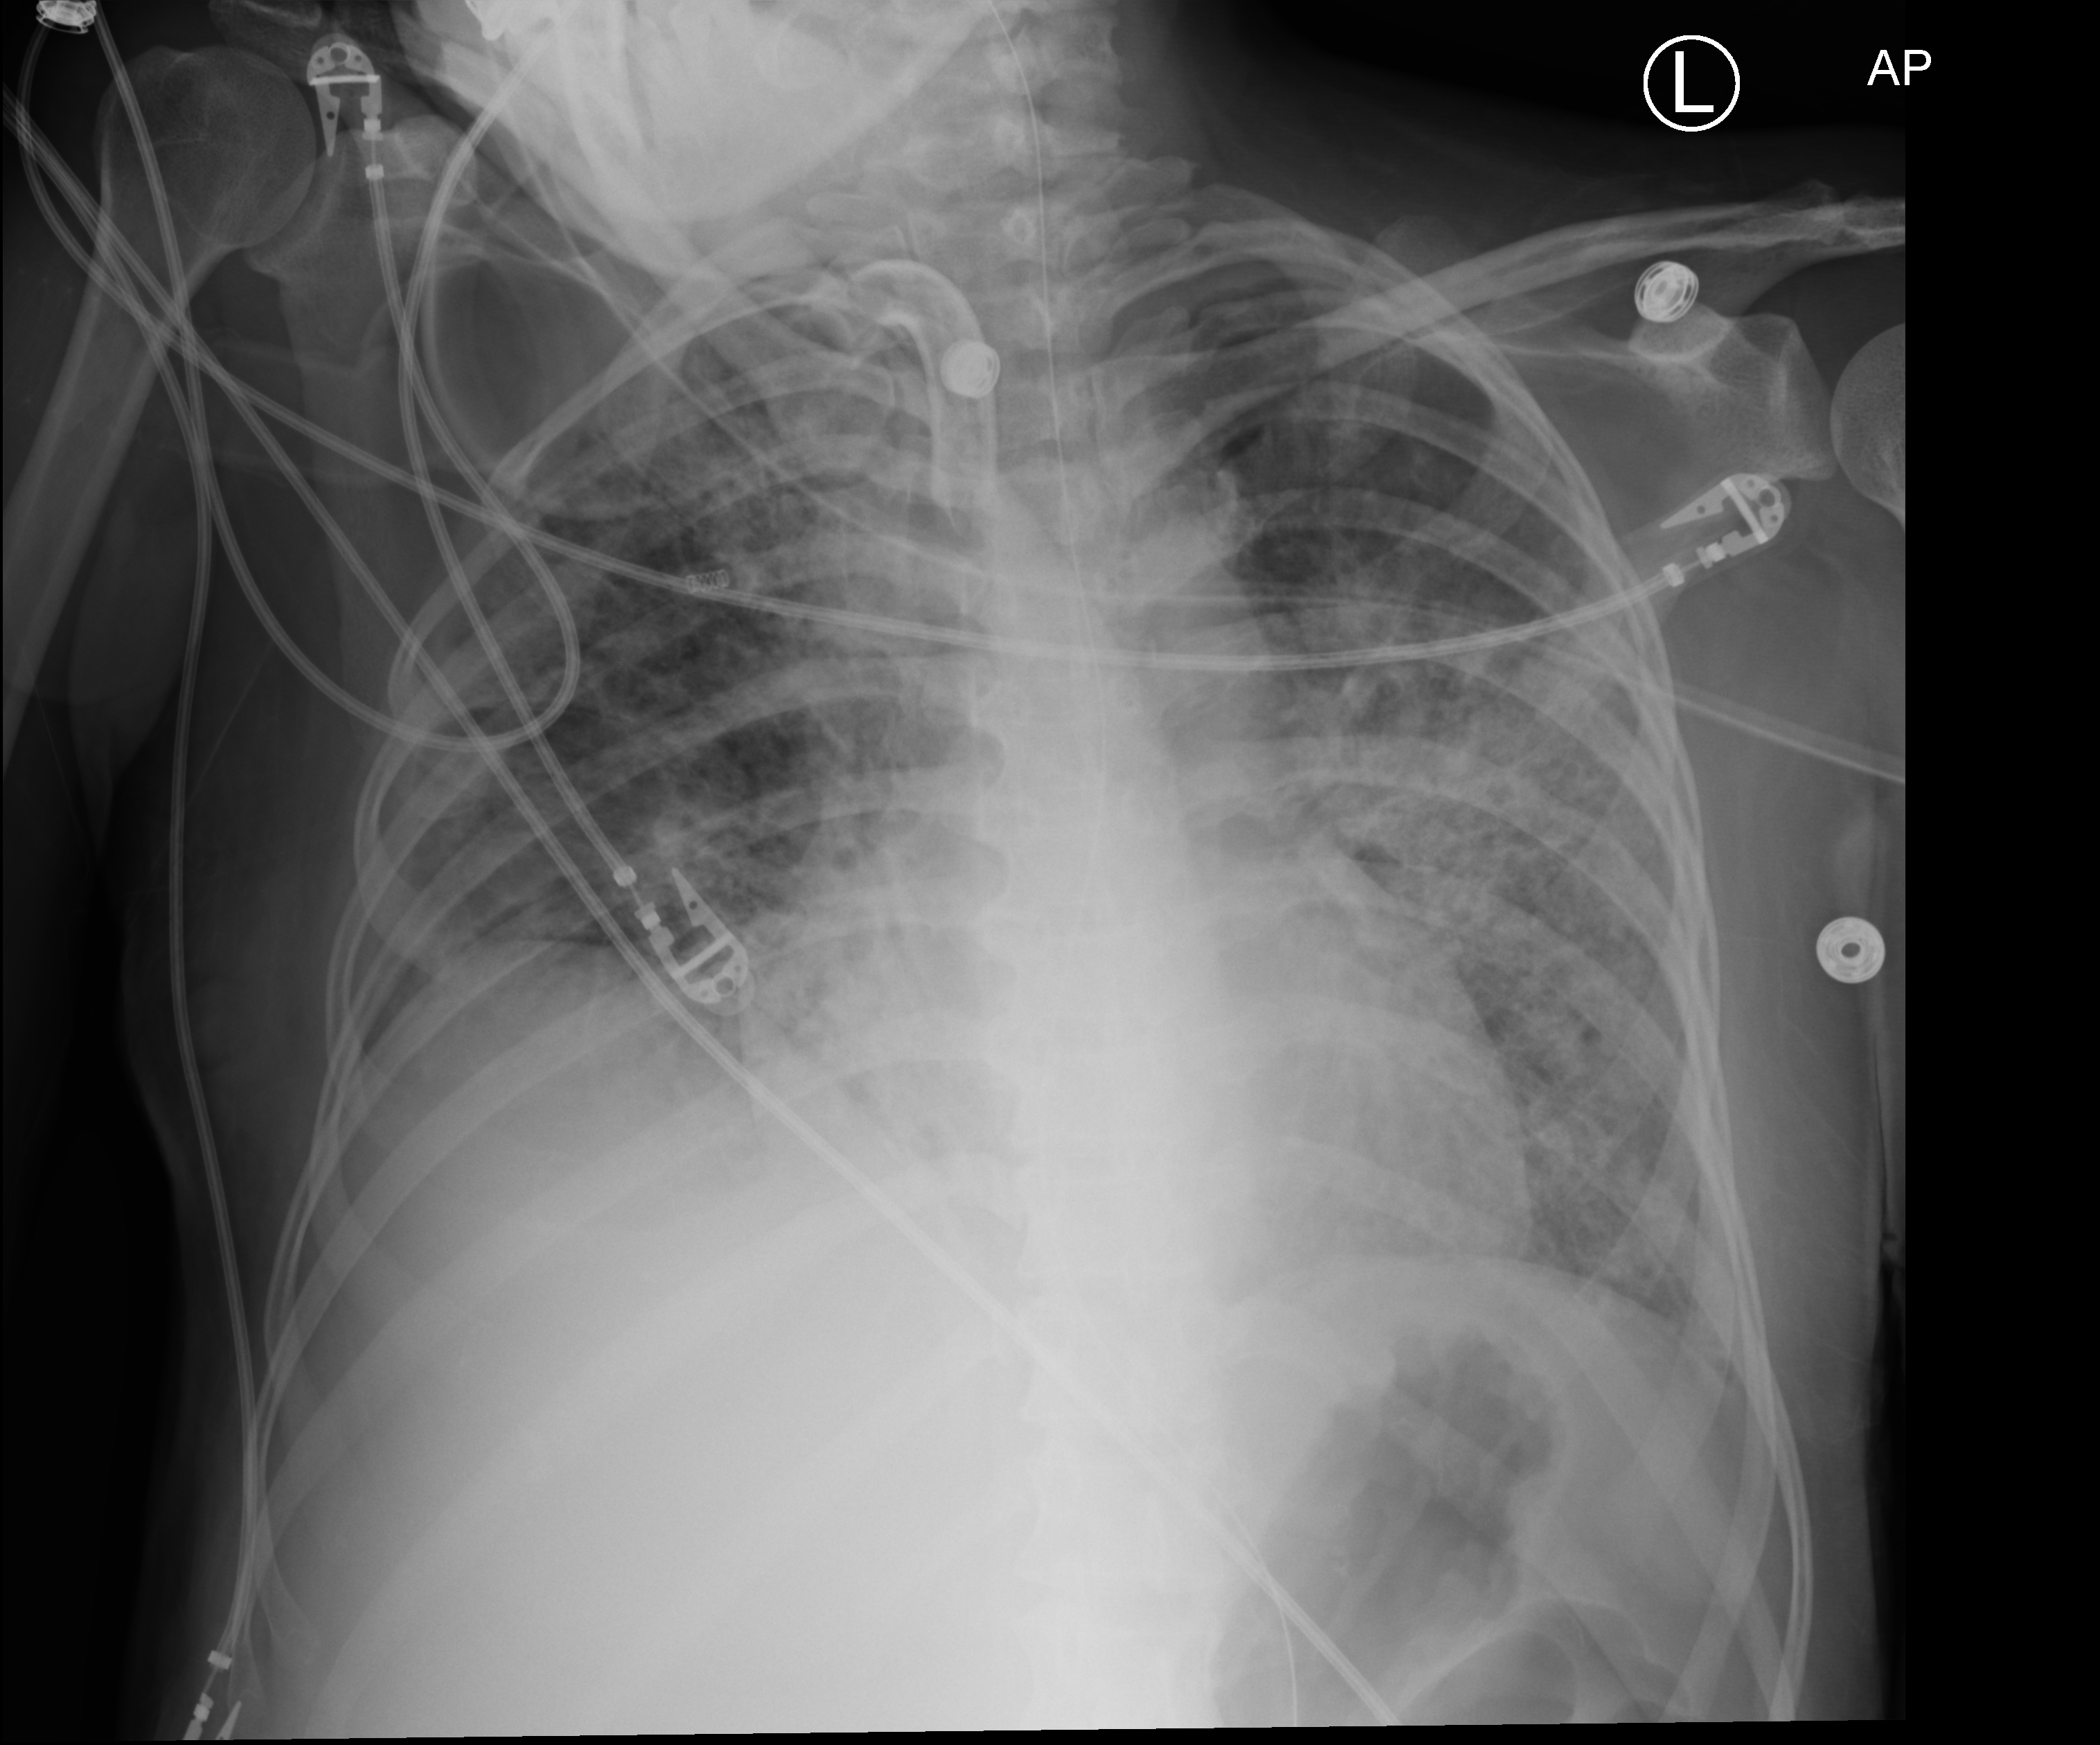
Portable chest radiograph. Patient hospitalised with COVID-19; female, aged 18–59 years.
From the hospital-stay record, not from the radiograph (when in the stay this image was taken is not recorded): admitted to intensive care during this hospital stay: yes.